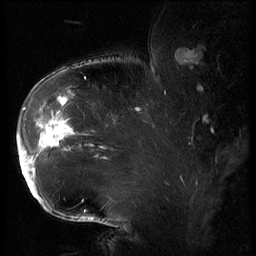
Breast MRI (dynamic contrast-enhanced), one sagittal slice. Position 44 of 62 along the scan axis. 3 images stored at this slice position (order not interpretable as contrast timing). 1.5 T. TE 4.2 ms, TR 9 ms. 256 × 256 image matrix, field of view 180 × 180 mm. Female patient, age 43 years. Case-level facts recorded for this patient, not image findings: setting: breast cancer imaged before/during neoadjuvant chemotherapy; receptor status: HER2-positive.
Outlined on this slice (semi-automatically segmented with operator editing):
- analysis volume of interest (the breast-tissue region the enhancement analysis was run in; not a lesion): bounding box (x1, y1, x2, y2) in pixels: (18, 90, 82, 203)
- tumour enhancement mask (voxels above the 140 % enhancement threshold inside the analysis volume of interest): (18, 98, 76, 196)